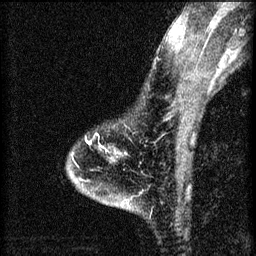
Breast MRI (dynamic contrast-enhanced), one sagittal slice. 3 images stored at this slice position (order not interpretable as contrast timing). 1.5 T. TE 4.2 ms, TR 8.2 ms. 256 × 256 image matrix. Female patient, age 46 years.
Outlined on this slice (semi-automatic segmentation, software-assisted and operator-edited):
- analysis volume of interest (the breast-tissue region the enhancement analysis was run in; not a lesion): bounding box (x1, y1, x2, y2) in pixels: (67, 140, 138, 209)
- tumour enhancement mask (voxels above the 70 % enhancement threshold inside the analysis volume of interest): (87, 142, 91, 145)